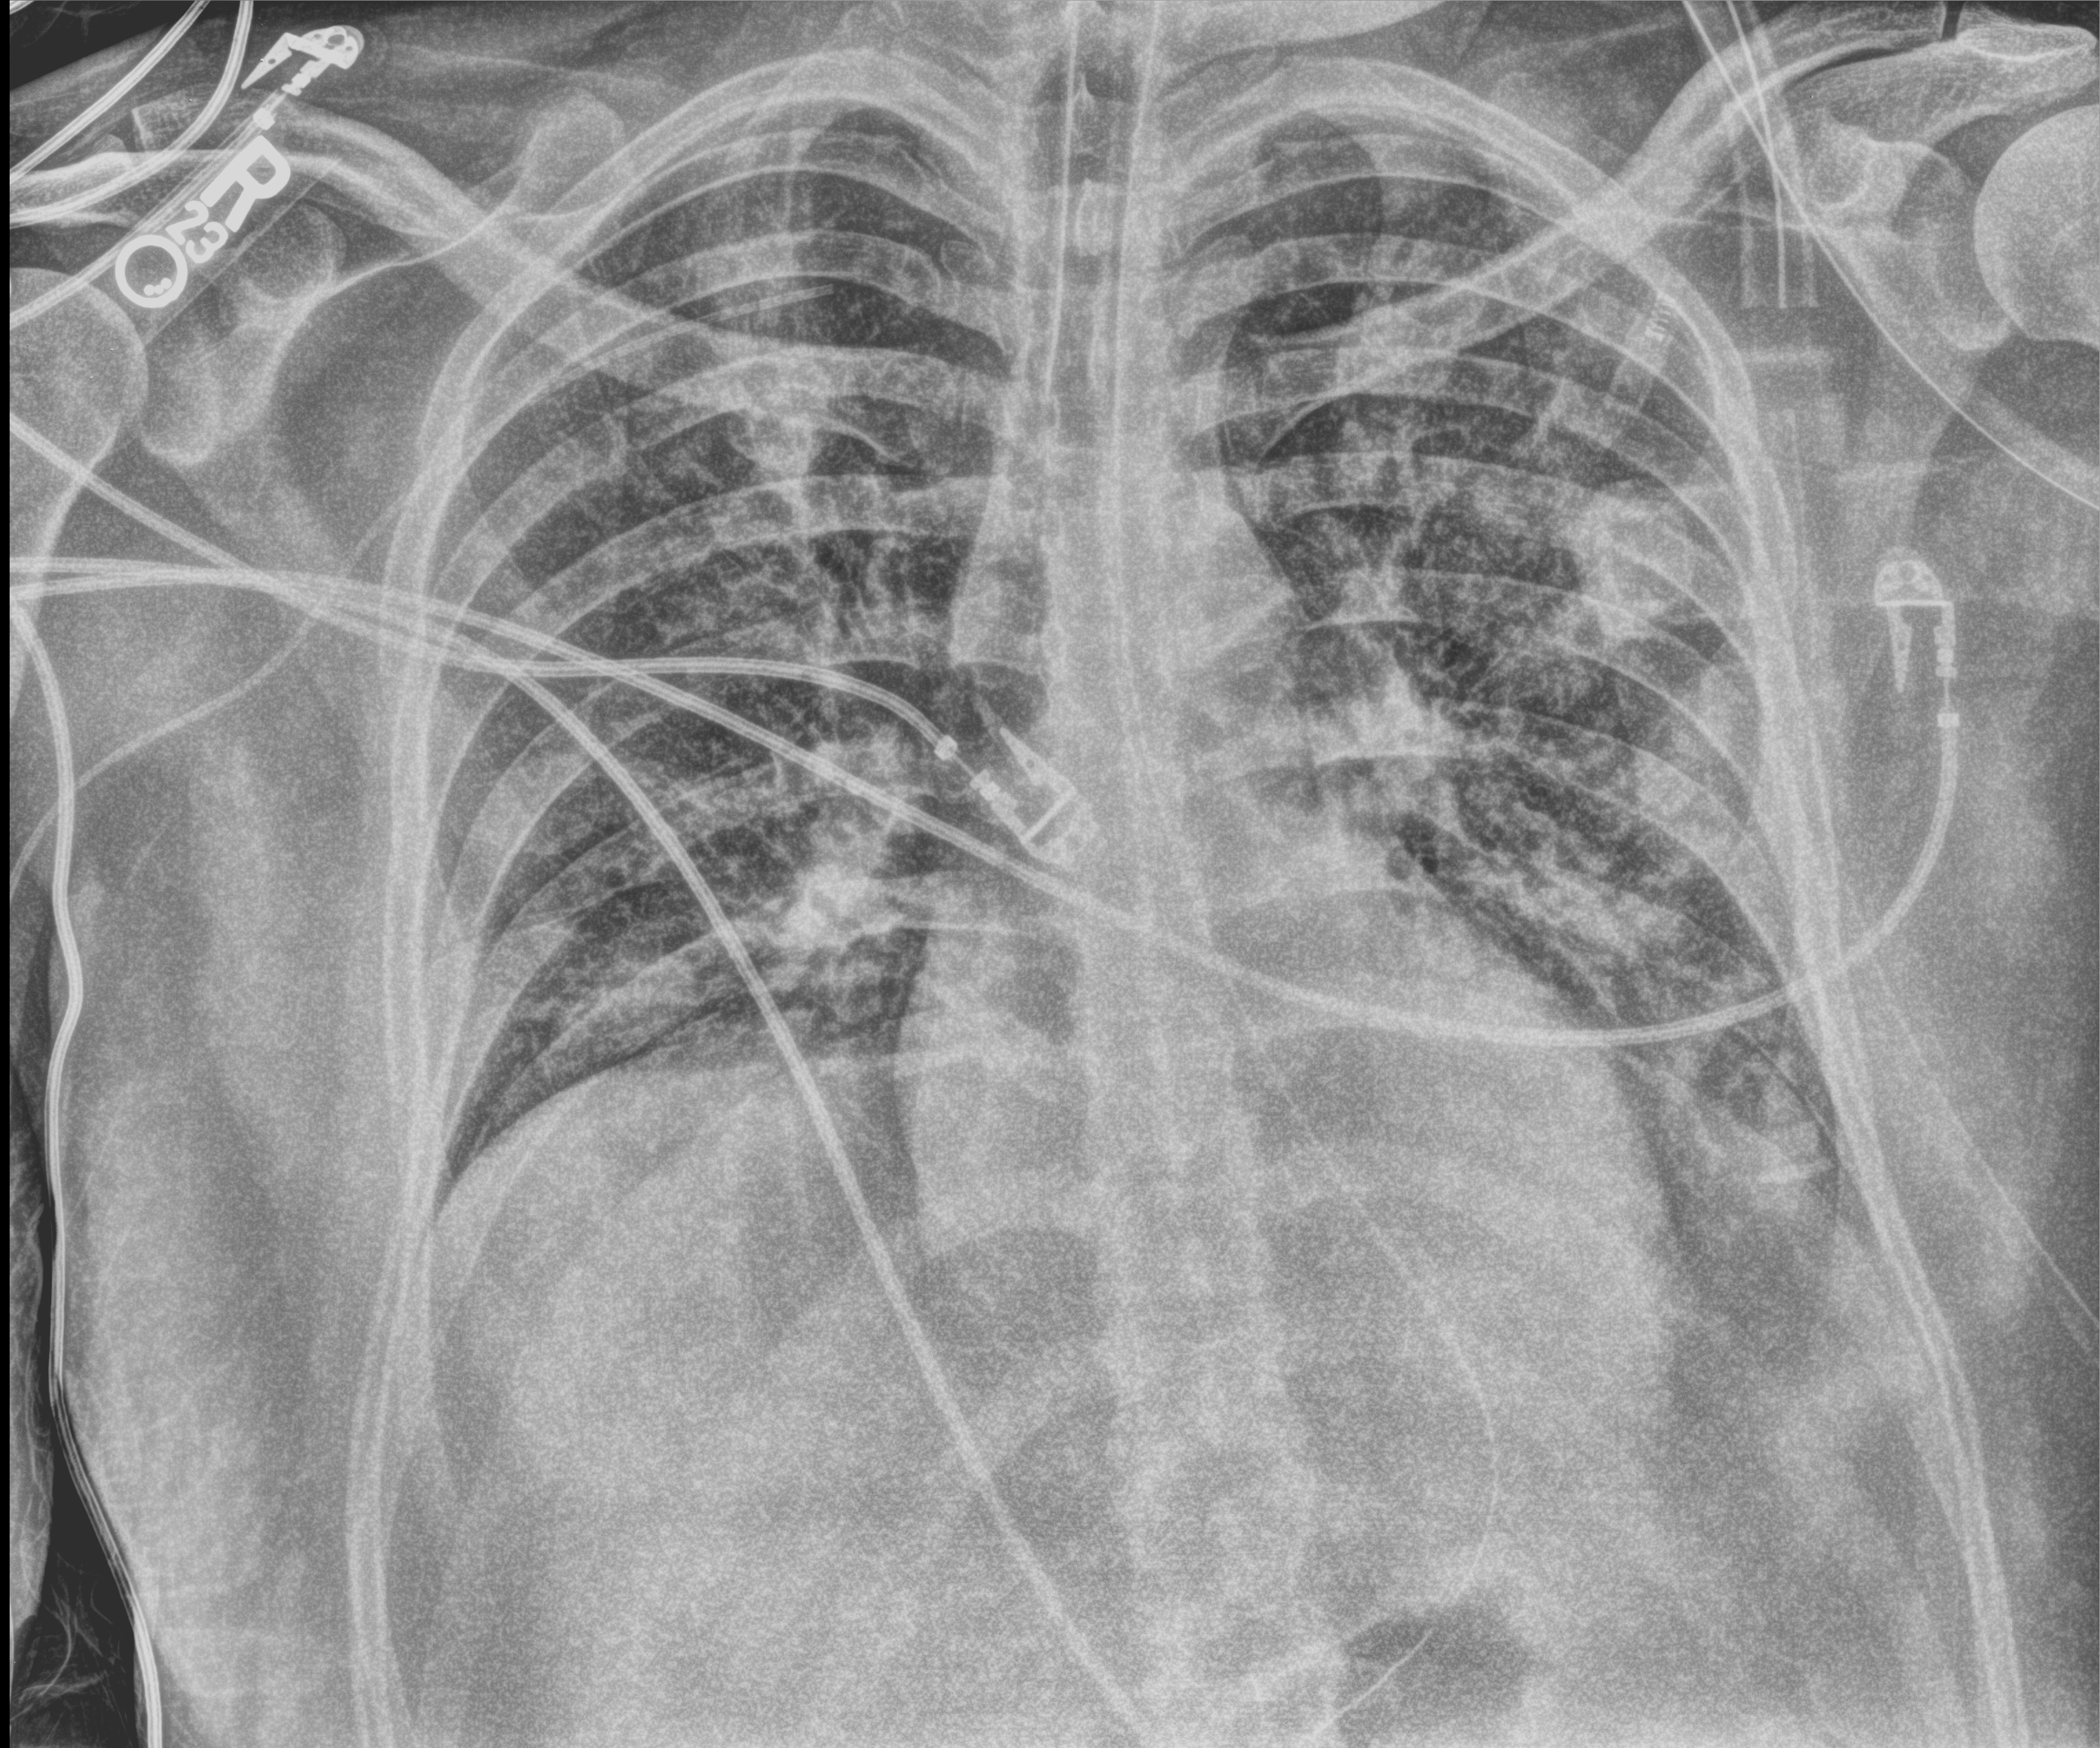
Bedside chest radiograph (computed radiography). Male patient hospitalised with COVID-19, age 18–59 years.
Admission-level facts for this patient (not findings on this image; timing relative to this image not recorded):
- admitted to intensive care during this hospital stay: yes
- chronic kidney disease (admission record): no
- mechanically ventilated during this hospital stay: yes